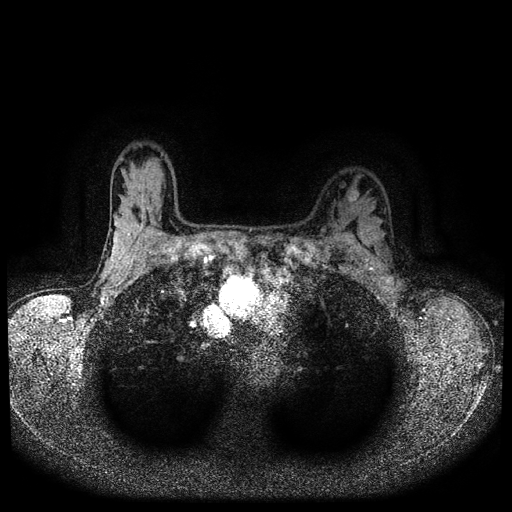
Breast MRI (dynamic contrast-enhanced, multi-phase), one axial slice. Position 76 of 116 along the scan axis. Dynamic contrast-enhanced series, time point 2 of 5 at this slice position (early post-contrast). 1.5 T. TE 2.7 ms, TR 5.4 ms. 2 mm slice thickness. 512 × 512 image matrix. Female patient, age 32 years.
Annotated regions visible in this slice (semi-automatically segmented with operator editing):
- breast lesion (labelled benign in the annotation): box from (x=345, y=187) to (x=360, y=207) px